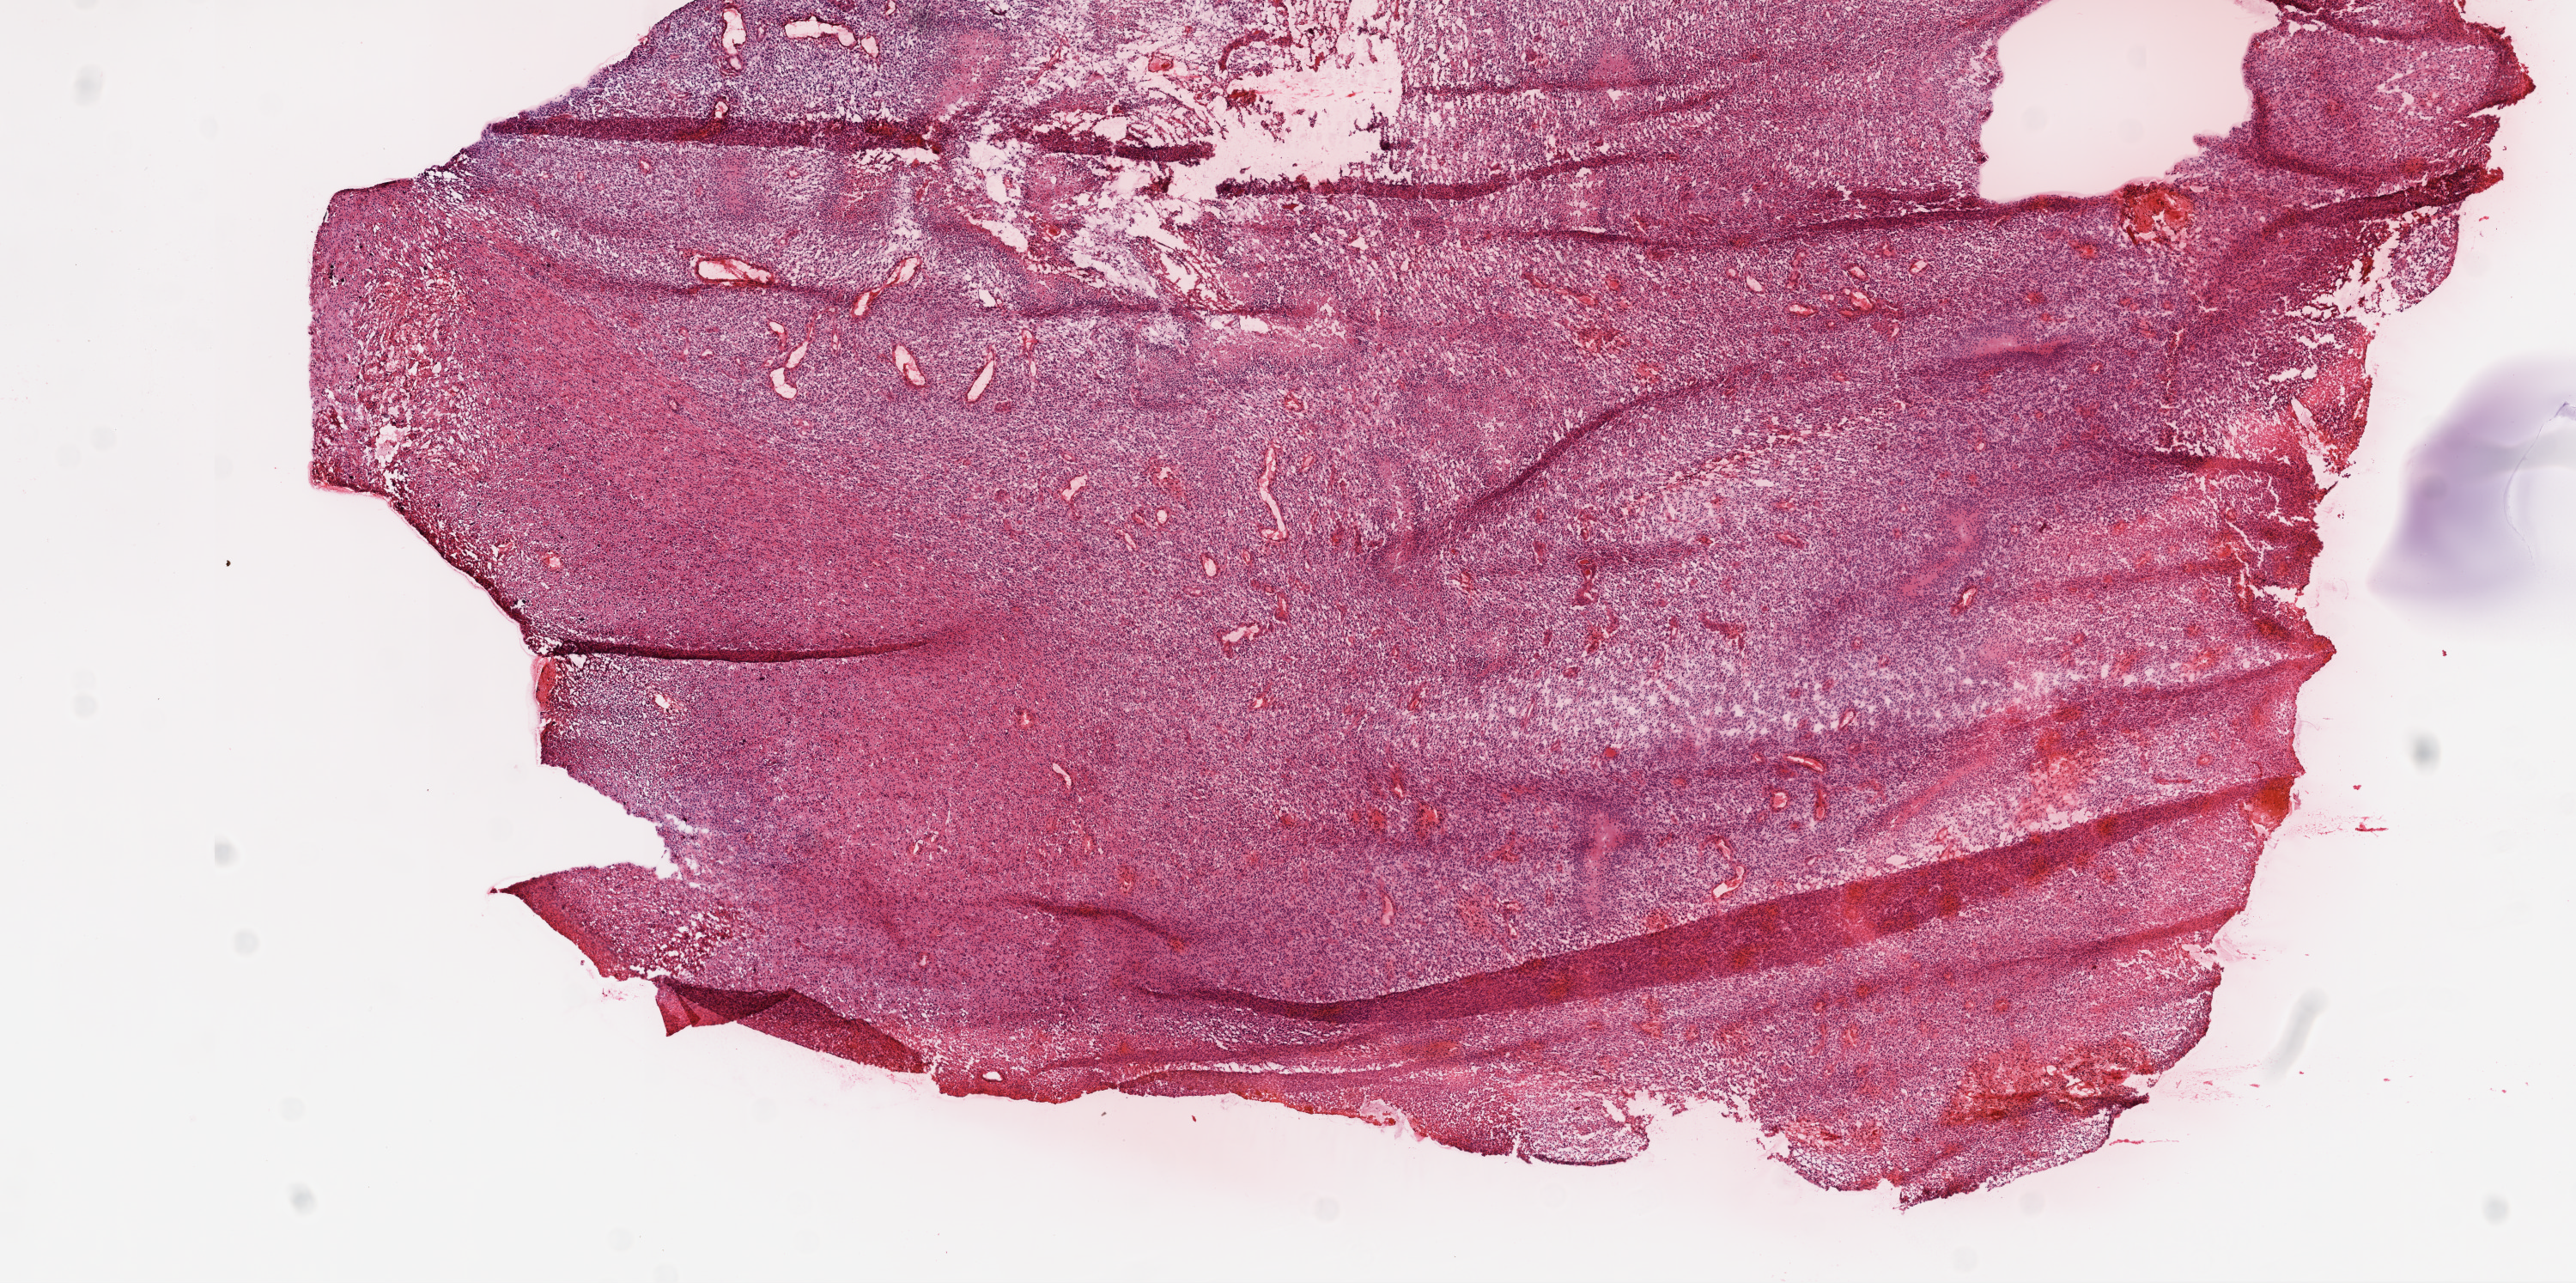
Whole-slide histology image, H&E — shown as a low-resolution overview of the whole scanned area (about 12.0 x 6.0 mm, from a 20x scan). Frozen section from the top of the tissue portion. Primary tumour sample from the brain. Patient: male, age at initial diagnosis 46 years. Pathologist review of this section (percent, as recorded): tumour cells 90%, tumour nuclei 85%, normal cells 0%, stromal cells 0%, necrosis 10%.
Pathologic diagnosis: Glioblastoma.